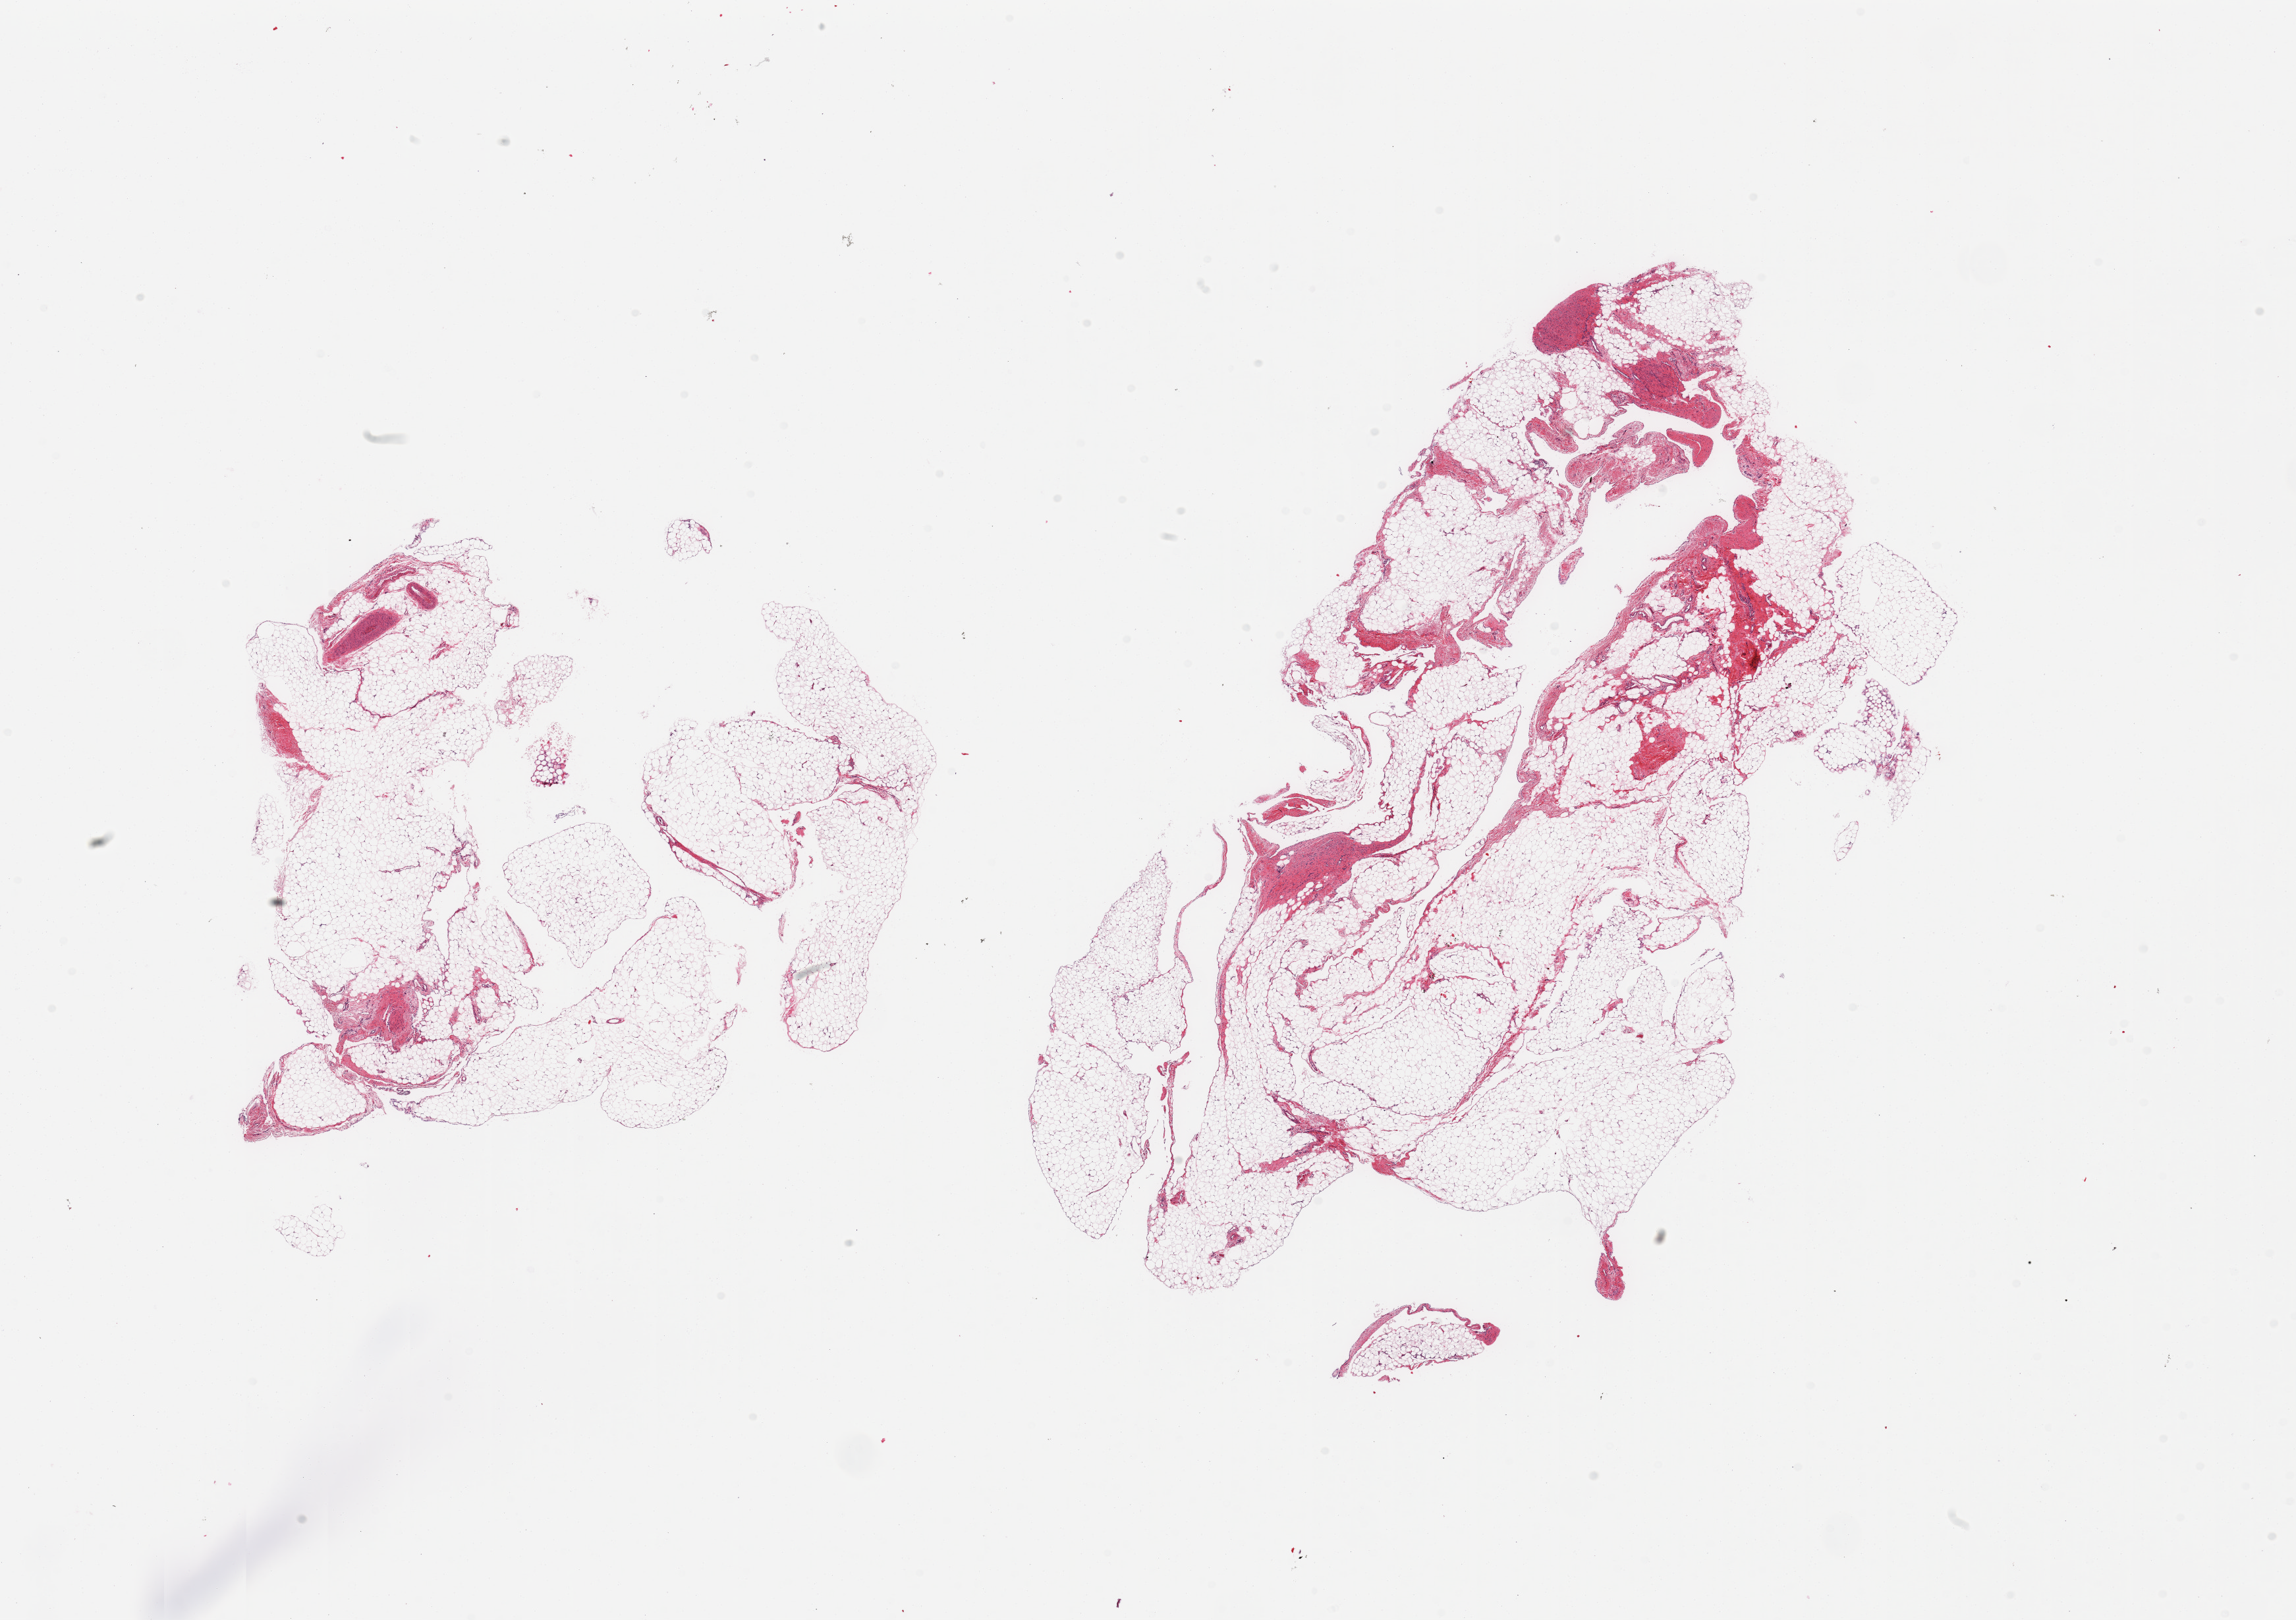
Whole-slide image, haematoxylin and eosin stain, brightfield — shown as a low-resolution overview of the whole scanned area (about 27.6 x 19.4 mm), PAXgene-fixed, paraffin-embedded tissue, section of omentum (target tissue), donor tissue sample. Donor sex: male.
* reviewer comment on this tissue sample: 2 pieces; lobulated fat with up to 10-20% fibrous component